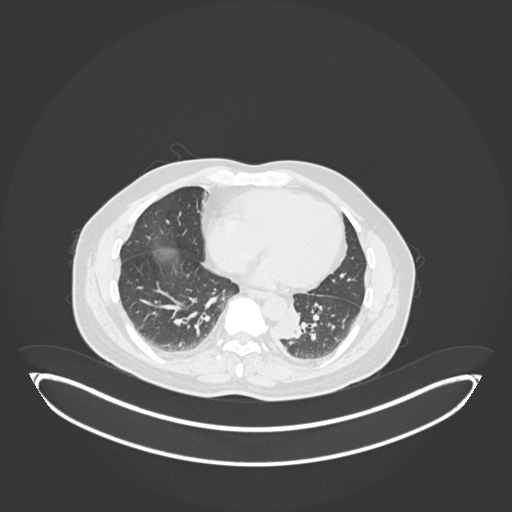
Chest CT, one axial slice. Slice 60 of 258 in the series (ordered by position). Lung window (W 1500 / L -600 HU). 1 mm slice thickness. 512 × 512 image matrix, field of view 500 × 500 mm. Patient: male, 54 years. From the clinical record (not read from this slice): clinical TNM (as recorded): T3 N0 M0.
Annotated regions visible in this slice (bounding box drawn by a radiologist):
- lung tumour (recorded histology: squamous cell carcinoma): bounding box (x1, y1, x2, y2) in pixels: (273, 311, 303, 343)